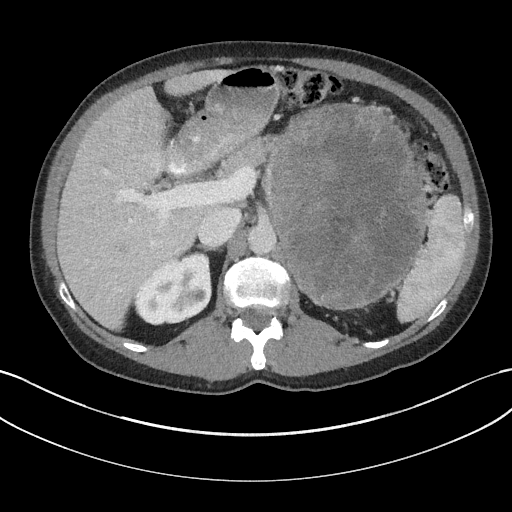
Contrast-enhanced abdominal CT, one axial slice; slice 112 of 147 in the series (ordered by position); reconstruction kernel I31f/3; 100 kVp; intravenous contrast given; soft-tissue window (W 400 / L 40 HU); 3 mm slice thickness; 512 × 512 image matrix, field of view 384 × 384 mm. Patient: male, 58 years. Case-level facts recorded for this patient, not image findings: diagnosis: adrenocortical carcinoma; tumour side: left adrenal; tumour size at pathology: 22 cm; Ki-67 index: 26 %; stage (as recorded): 2.
Annotated regions visible in this slice (semi-automatic segmentation, software-assisted and operator-edited):
- mass: box from (x=272, y=105) to (x=423, y=306) px